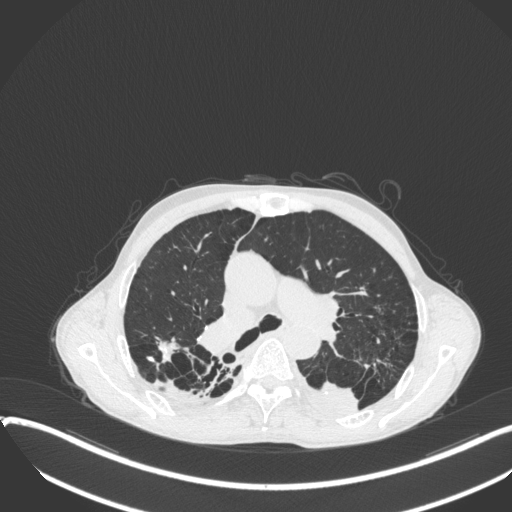
Chest CT, one axial slice. Slice 251 of 400 in the series (ordered by position). 120 kVp. Lung window (W 1500 / L -600 HU). 1 mm slice thickness. 512 × 512 image matrix. Patient: male, 57 years. Case-level facts recorded for this patient, not image findings: clinical TNM (as recorded): T4 N0 M0.
Annotated regions visible in this slice (rectangle marked by the reading radiologist):
- lung tumour (recorded histology: squamous cell carcinoma): box from (x=302, y=376) to (x=362, y=420) px